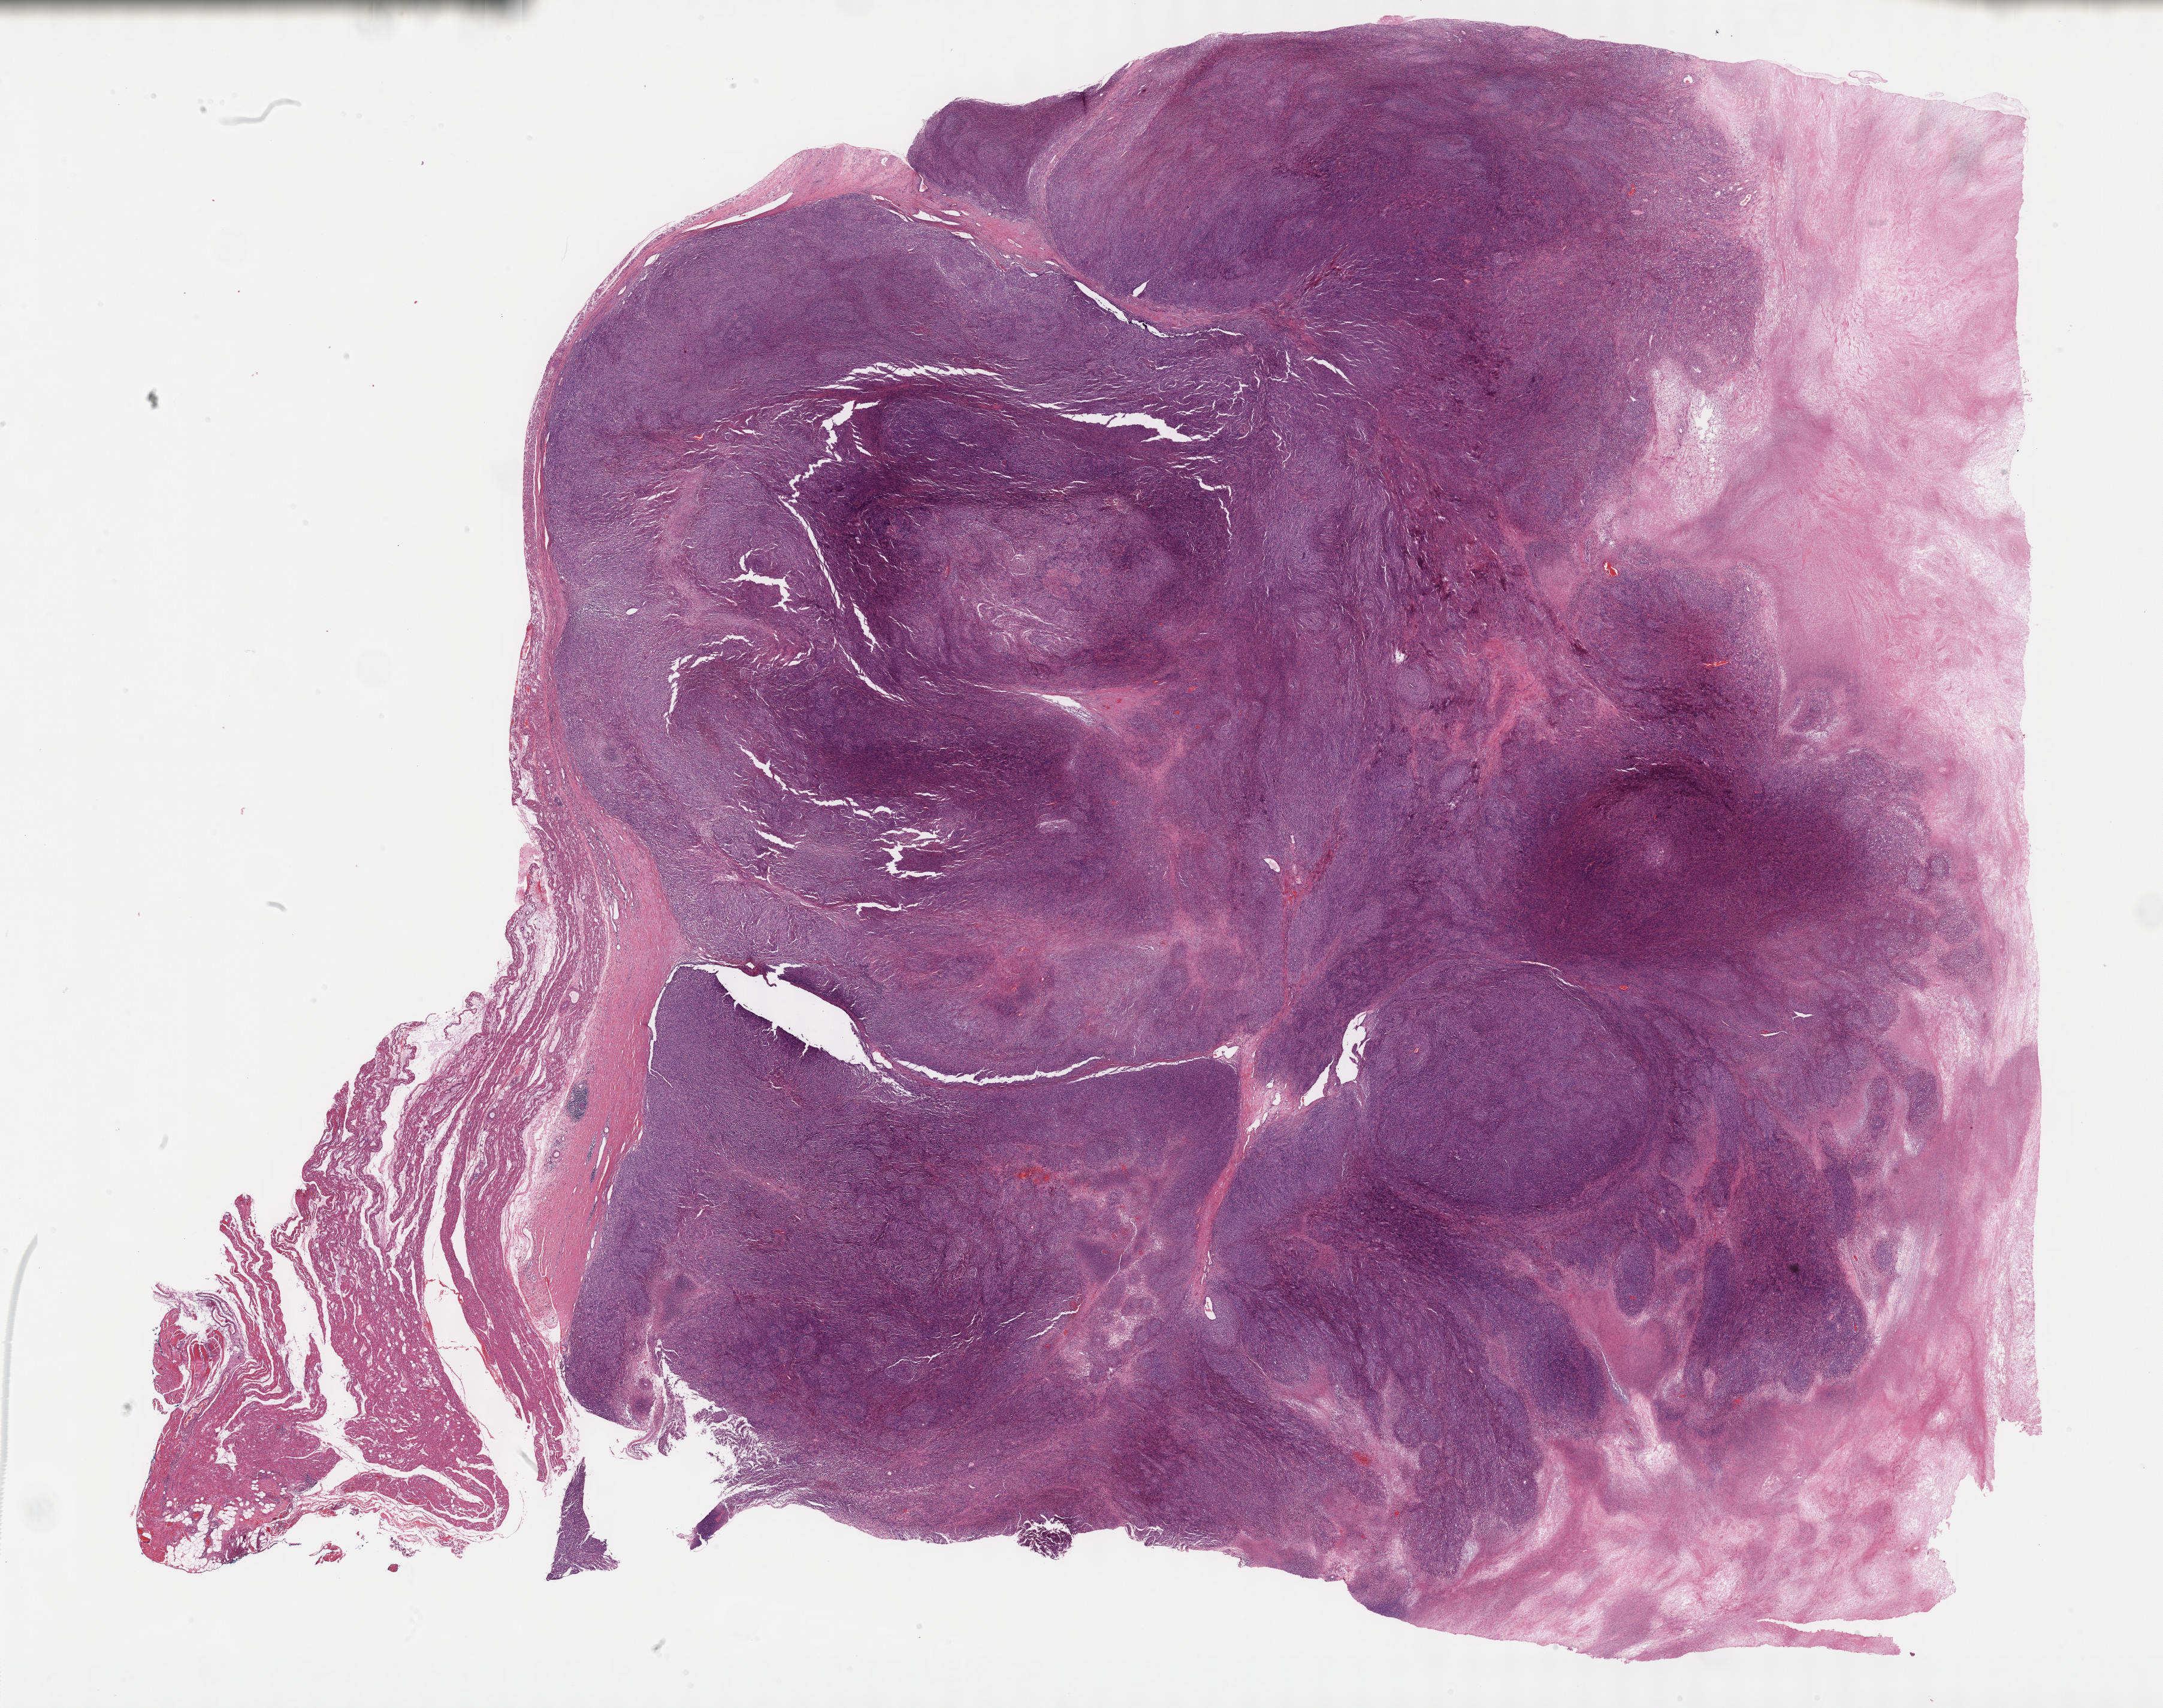
Digitized H&E tissue section (whole slide), whole scanned area (about 29.2 x 23.1 mm, from a 40x scan) shown as a low-resolution overview; formalin-fixed paraffin-embedded (FFPE) diagnostic section; sample: primary tumour, retroperitoneum and peritoneum. Male patient; age at initial diagnosis 55 years.
* diagnosis: Undifferentiated sarcoma (retroperitoneum)